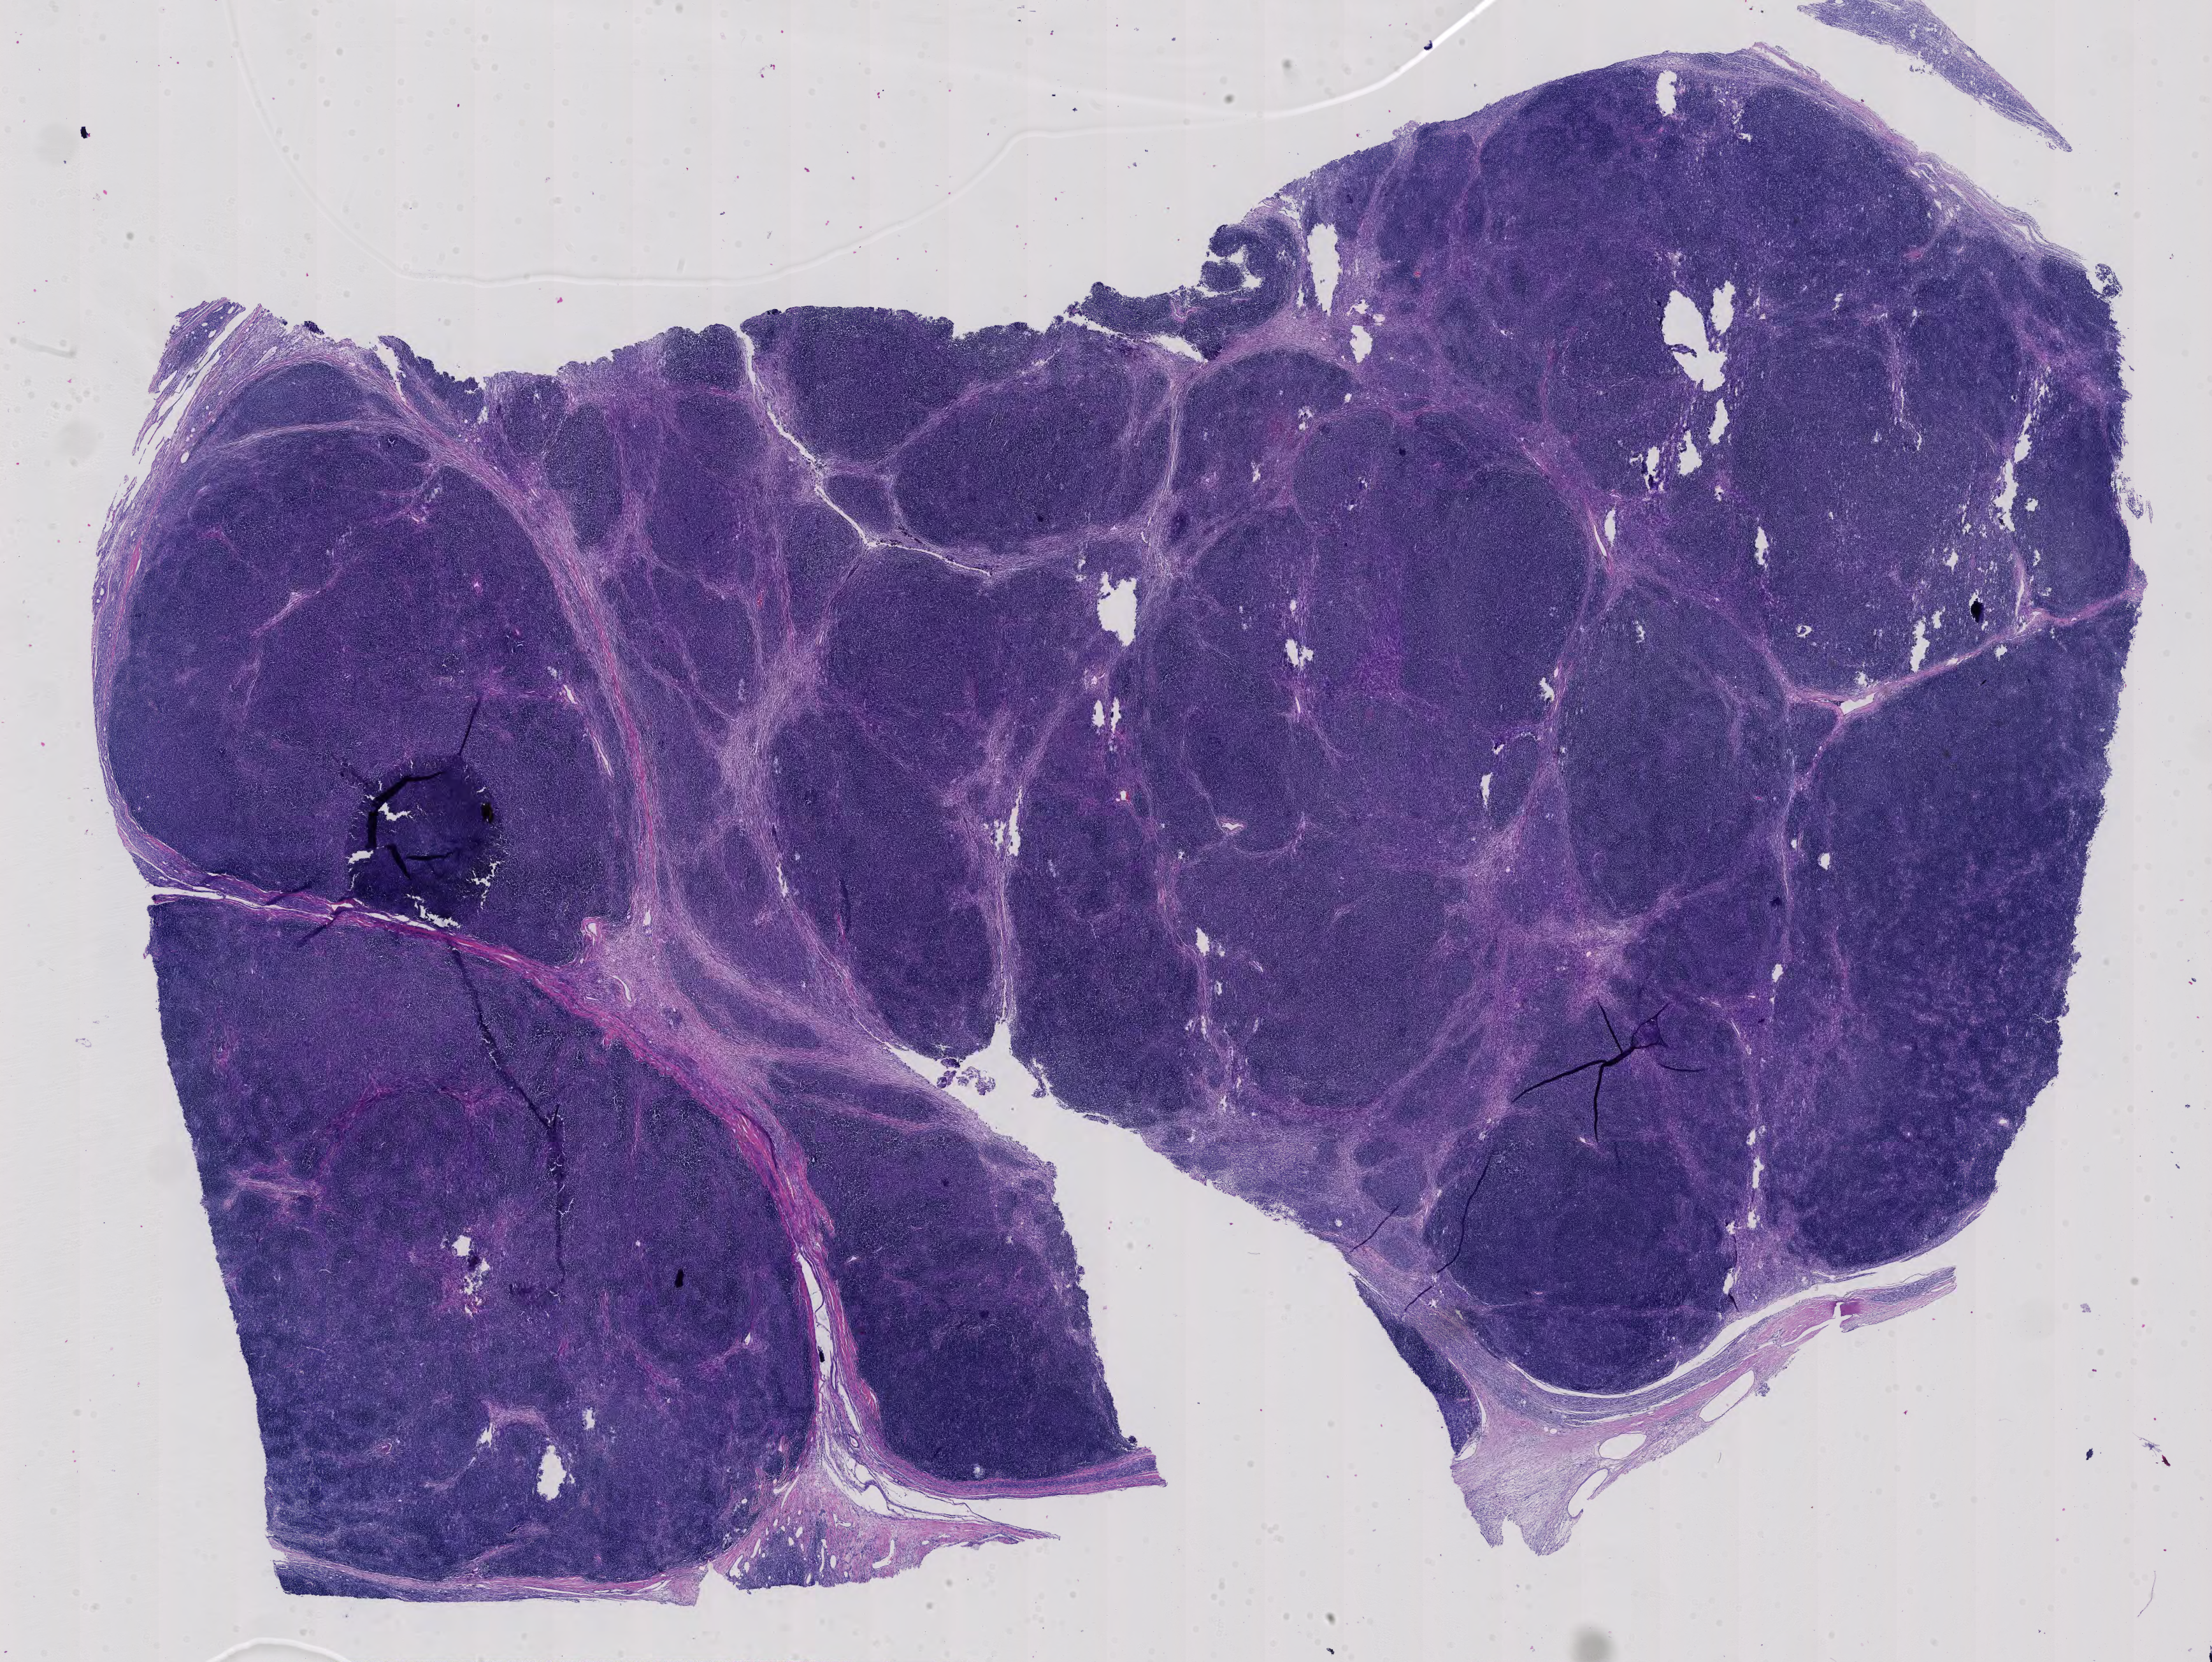
Digitized H&E tissue section (whole slide) — a low-resolution overview of the entire scanned area, about 25.3 x 19.0 mm (acquisition: 40x scan). Formalin-fixed paraffin-embedded (FFPE) diagnostic section. Thymus, primary tumour sample. Patient: female, age at initial diagnosis 56 years.
Diagnosis: Thymoma, type AB, malignant (anterior mediastinum).